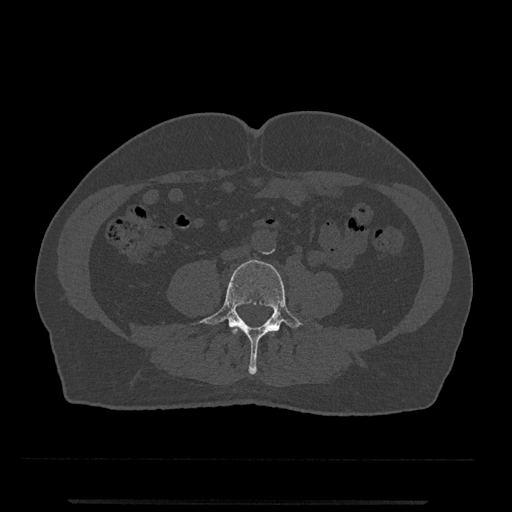
CT including the spine, one axial slice. Position 142 of 797 along the scan axis. 120 kVp. Bone window (W 1800 / L 400 HU). 0.5 mm slice thickness. 512 × 512 image matrix, field of view 419 × 419 mm. Male patient, age 63 years. From the clinical record (not read from this slice): primary cancer: prostate.
Structures marked on this image (semi-automatic segmentation, software-assisted and operator-edited):
- L3 vertebra: bounding box <231,327,275,336> (left, top, right, bottom; pixels)
- L4 vertebra: <191,260,305,374>